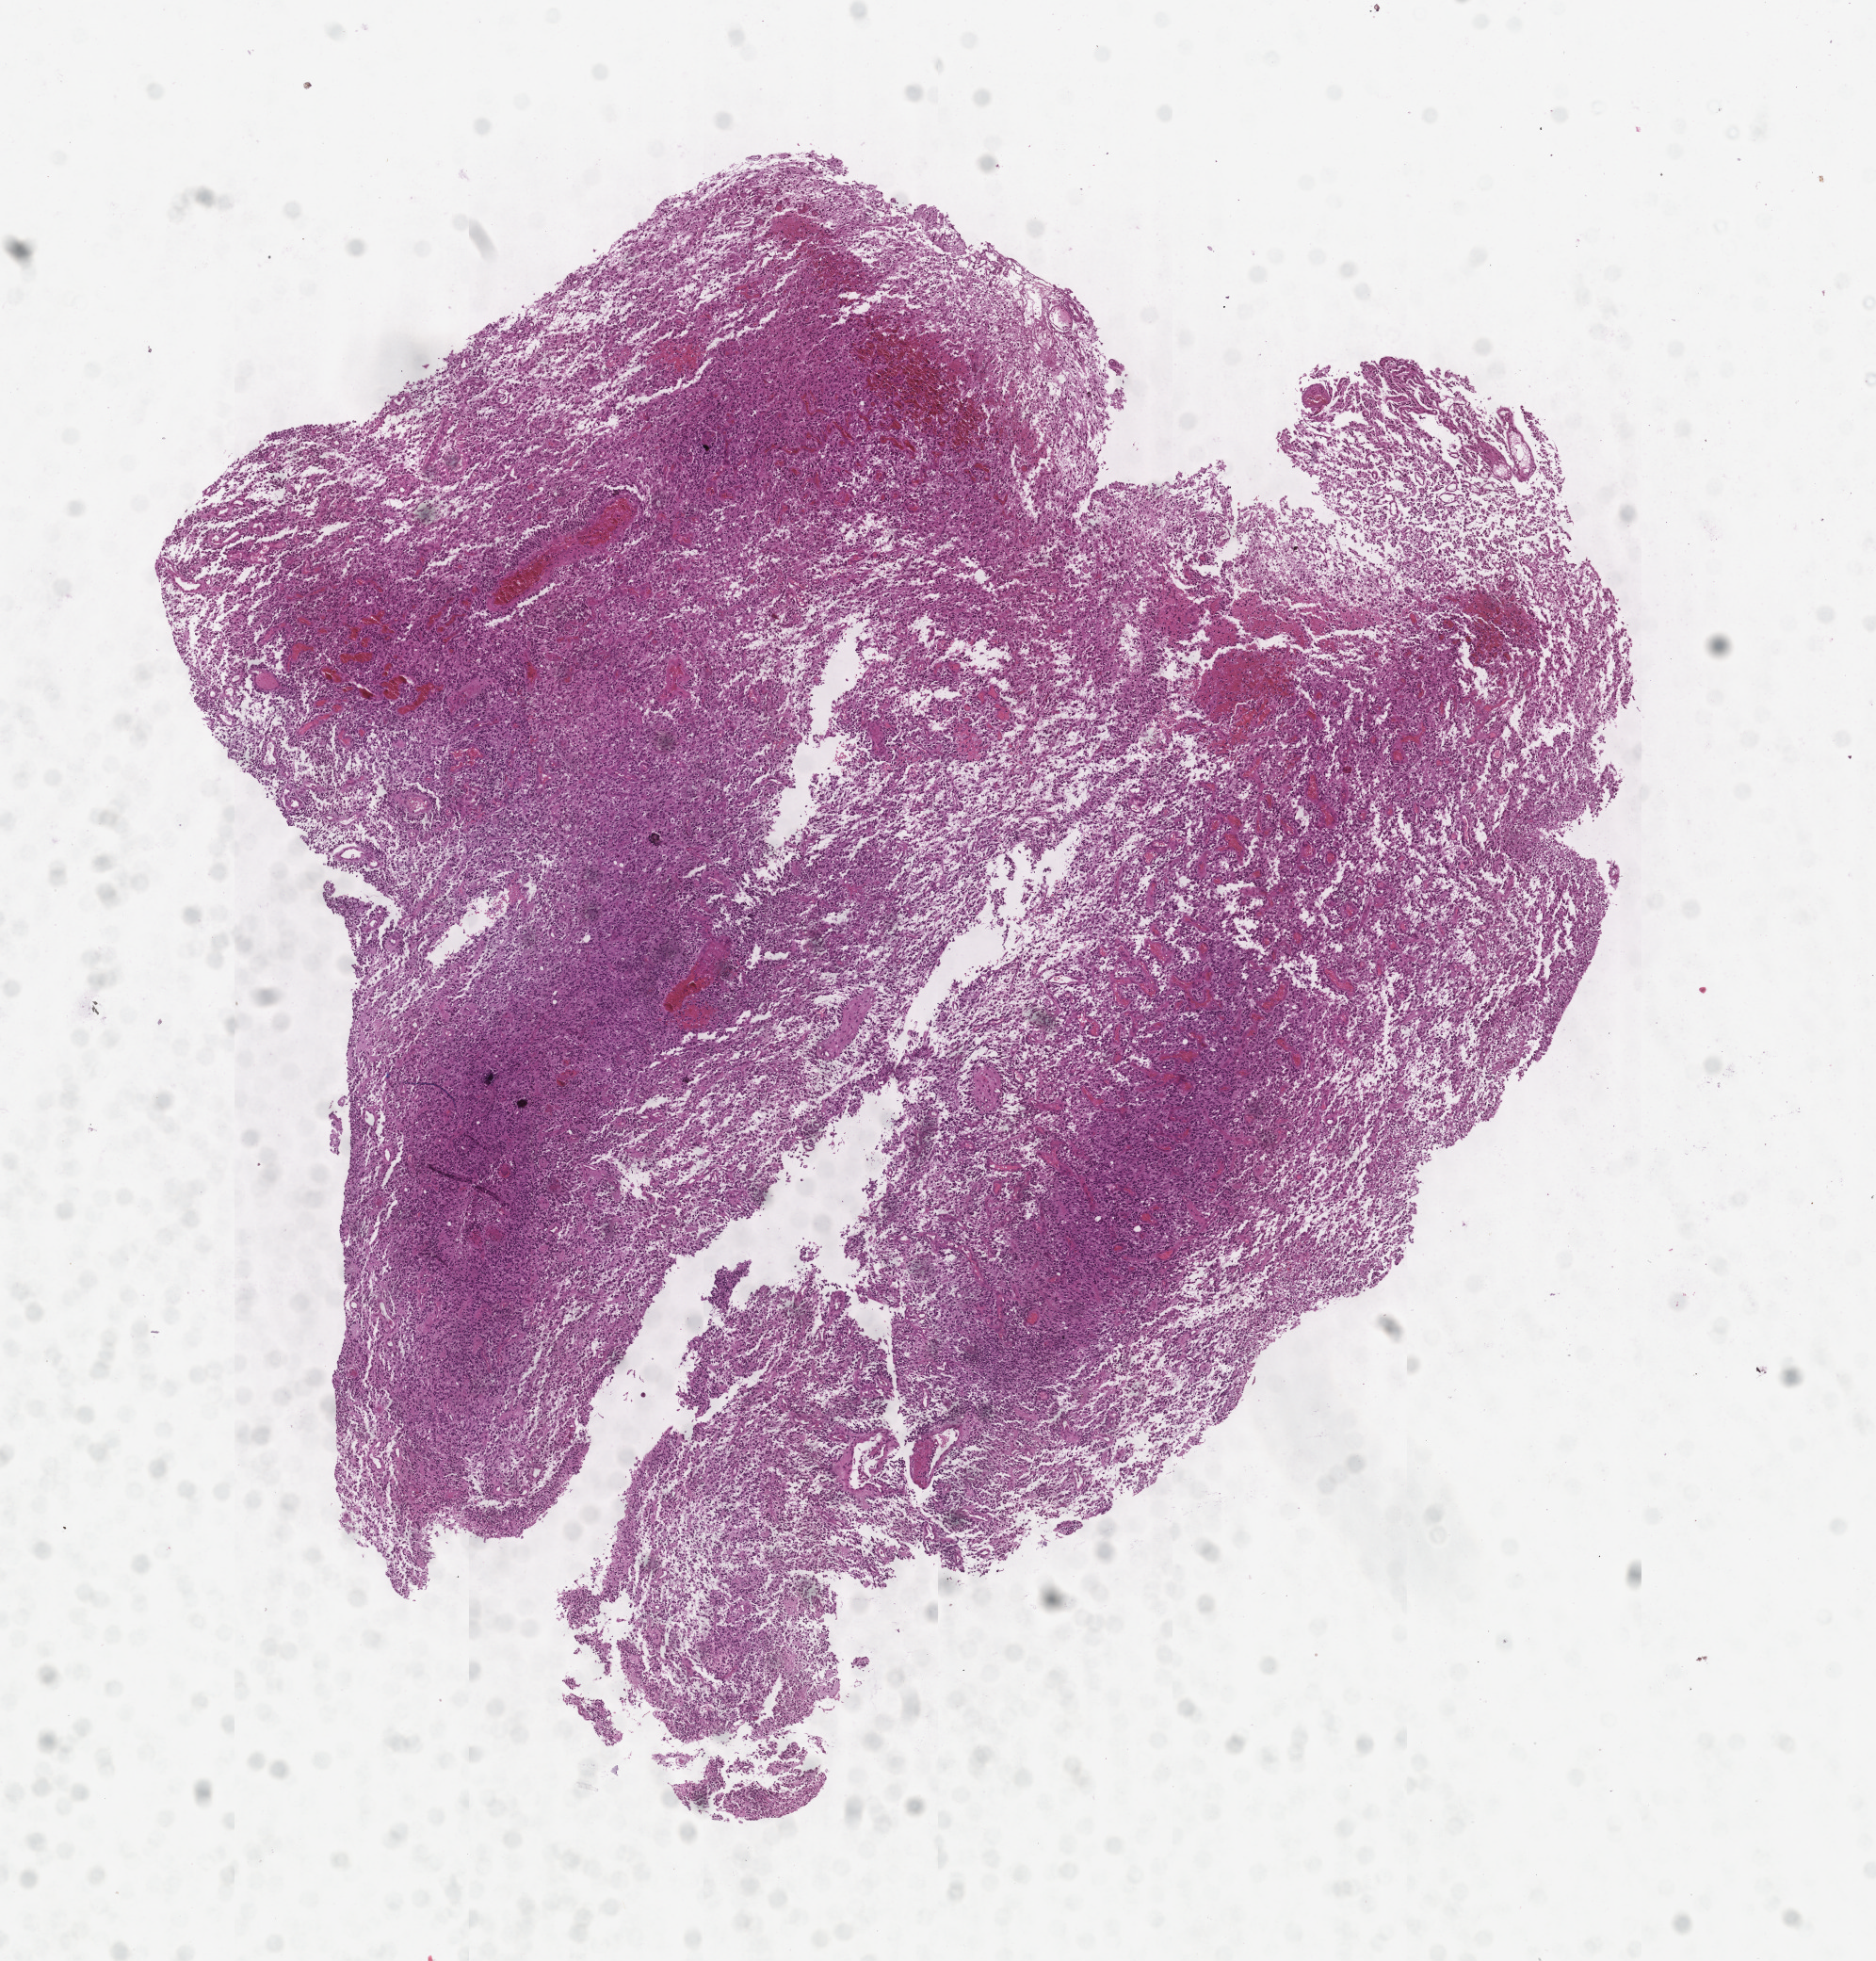
Hematoxylin and eosin (H&E) stained whole-slide image, shown as a low-resolution overview of the whole scanned area (about 8.0 x 8.4 mm, slide scanned at 20x). Tumour tissue sample, sampled site: brain. 63-year-old female patient. Pathologist review of this section (percent, as recorded): tumour nuclei 65%, necrosis 10%.
Histologic diagnosis: Glioblastoma.